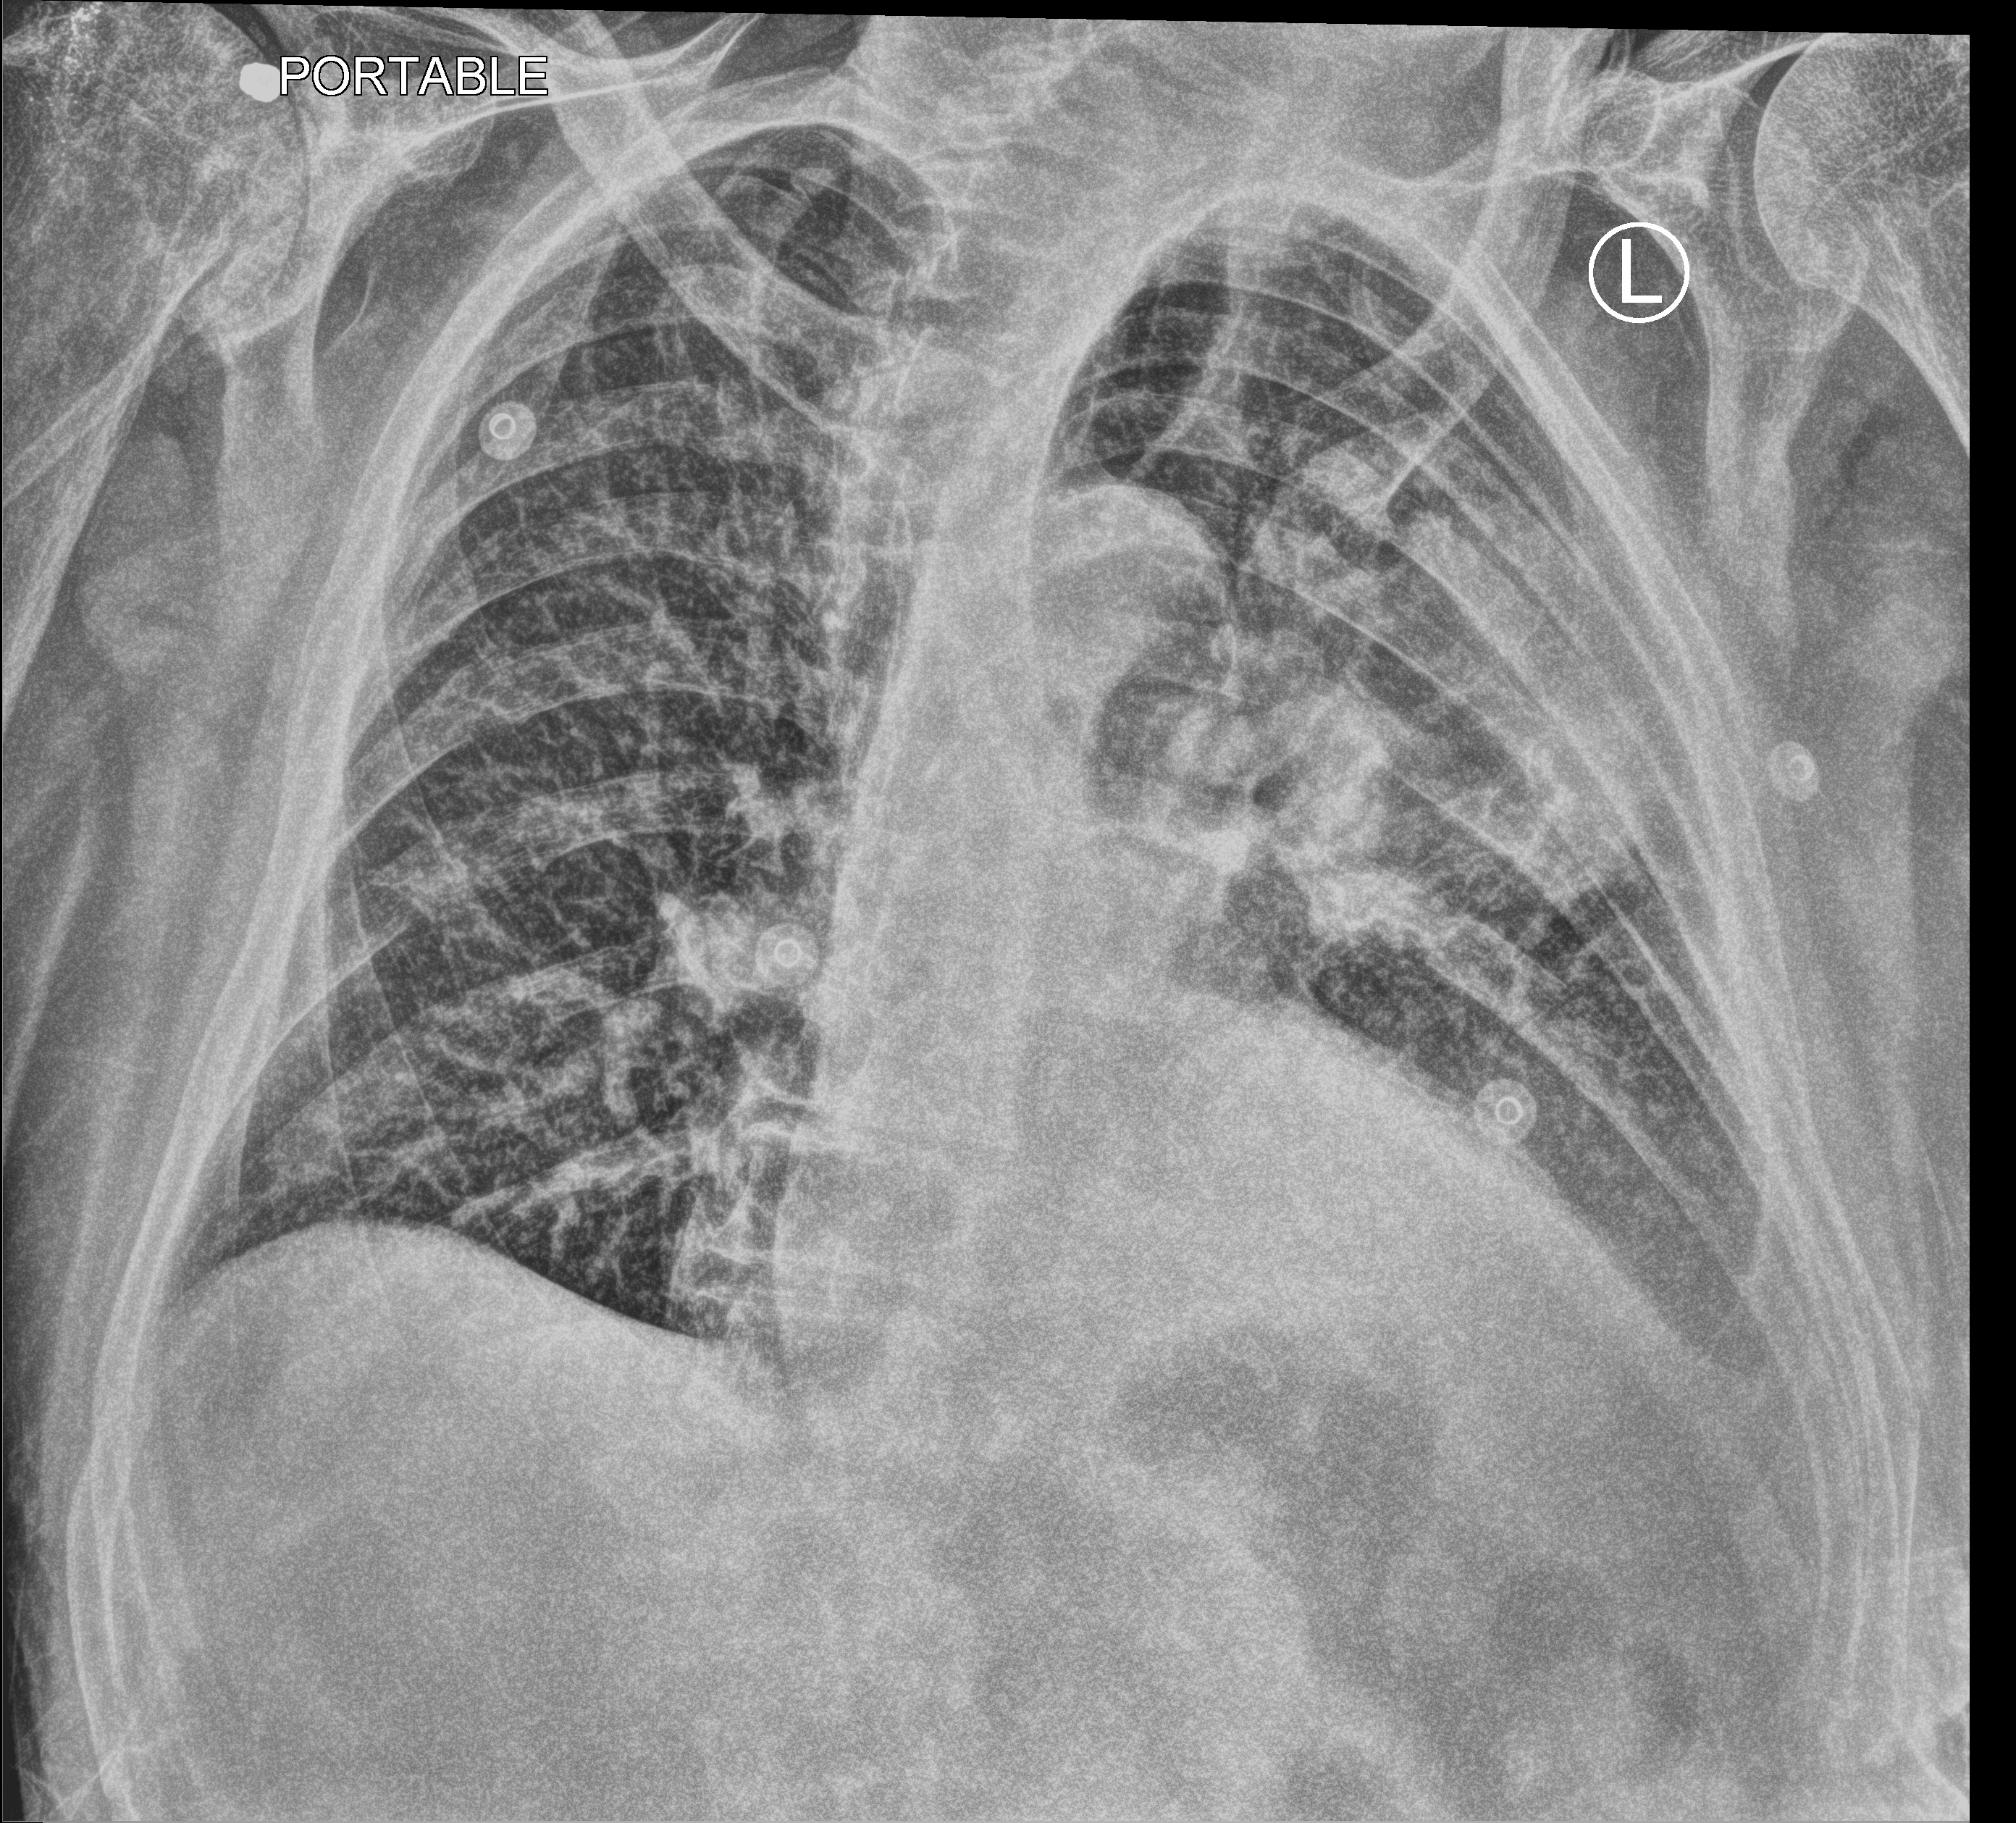
Portable chest radiograph; anteroposterior (AP) projection. Male patient hospitalised with COVID-19, age 75–90 years.
Hospital-stay facts (about this admission, not read from this image; timing relative to this image not recorded): smoking status (admission record): former; mechanically ventilated during this hospital stay: no.